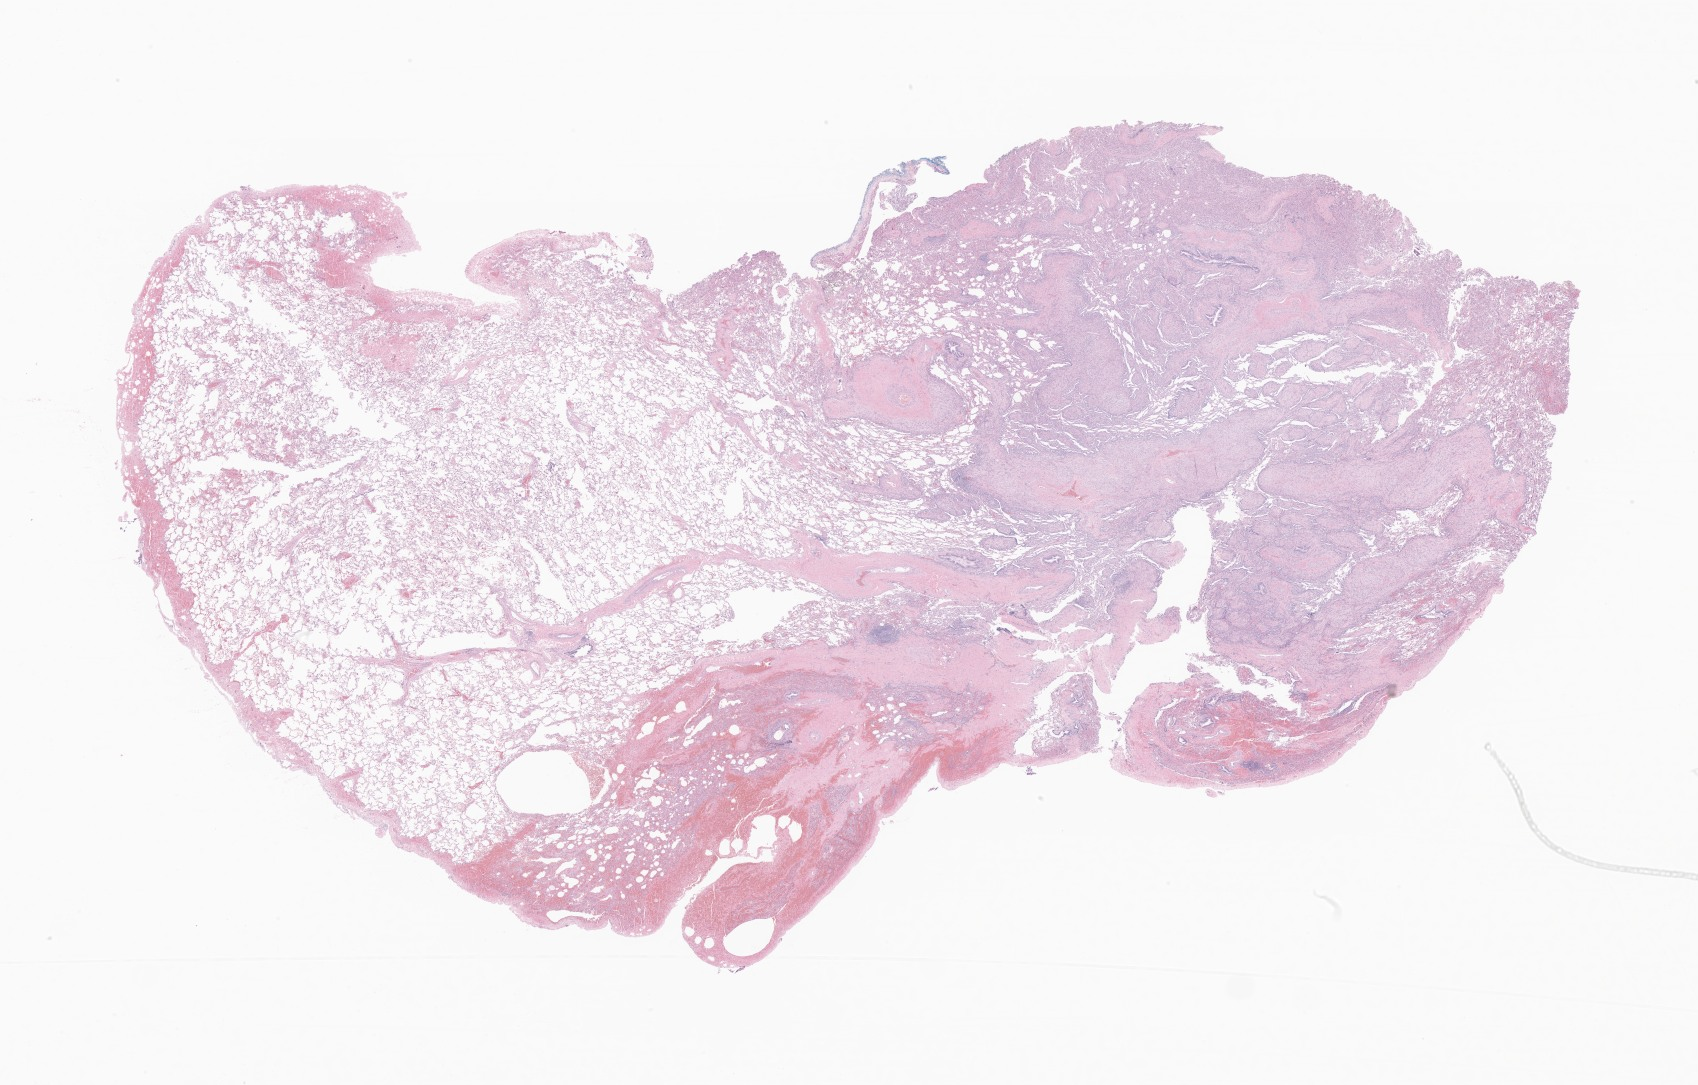
Digitized hematoxylin and eosin (H&E)-stained section of tumor tissue from the lower lobe of lung — a low-resolution overview of the entire scanned area, about 28.6 x 18.3 mm; formalin-fixed, paraffin-embedded (FFPE) tissue. Patient: male, age 182 months.
Recorded diagnosis: Myofibroblastic tumor, NOS.